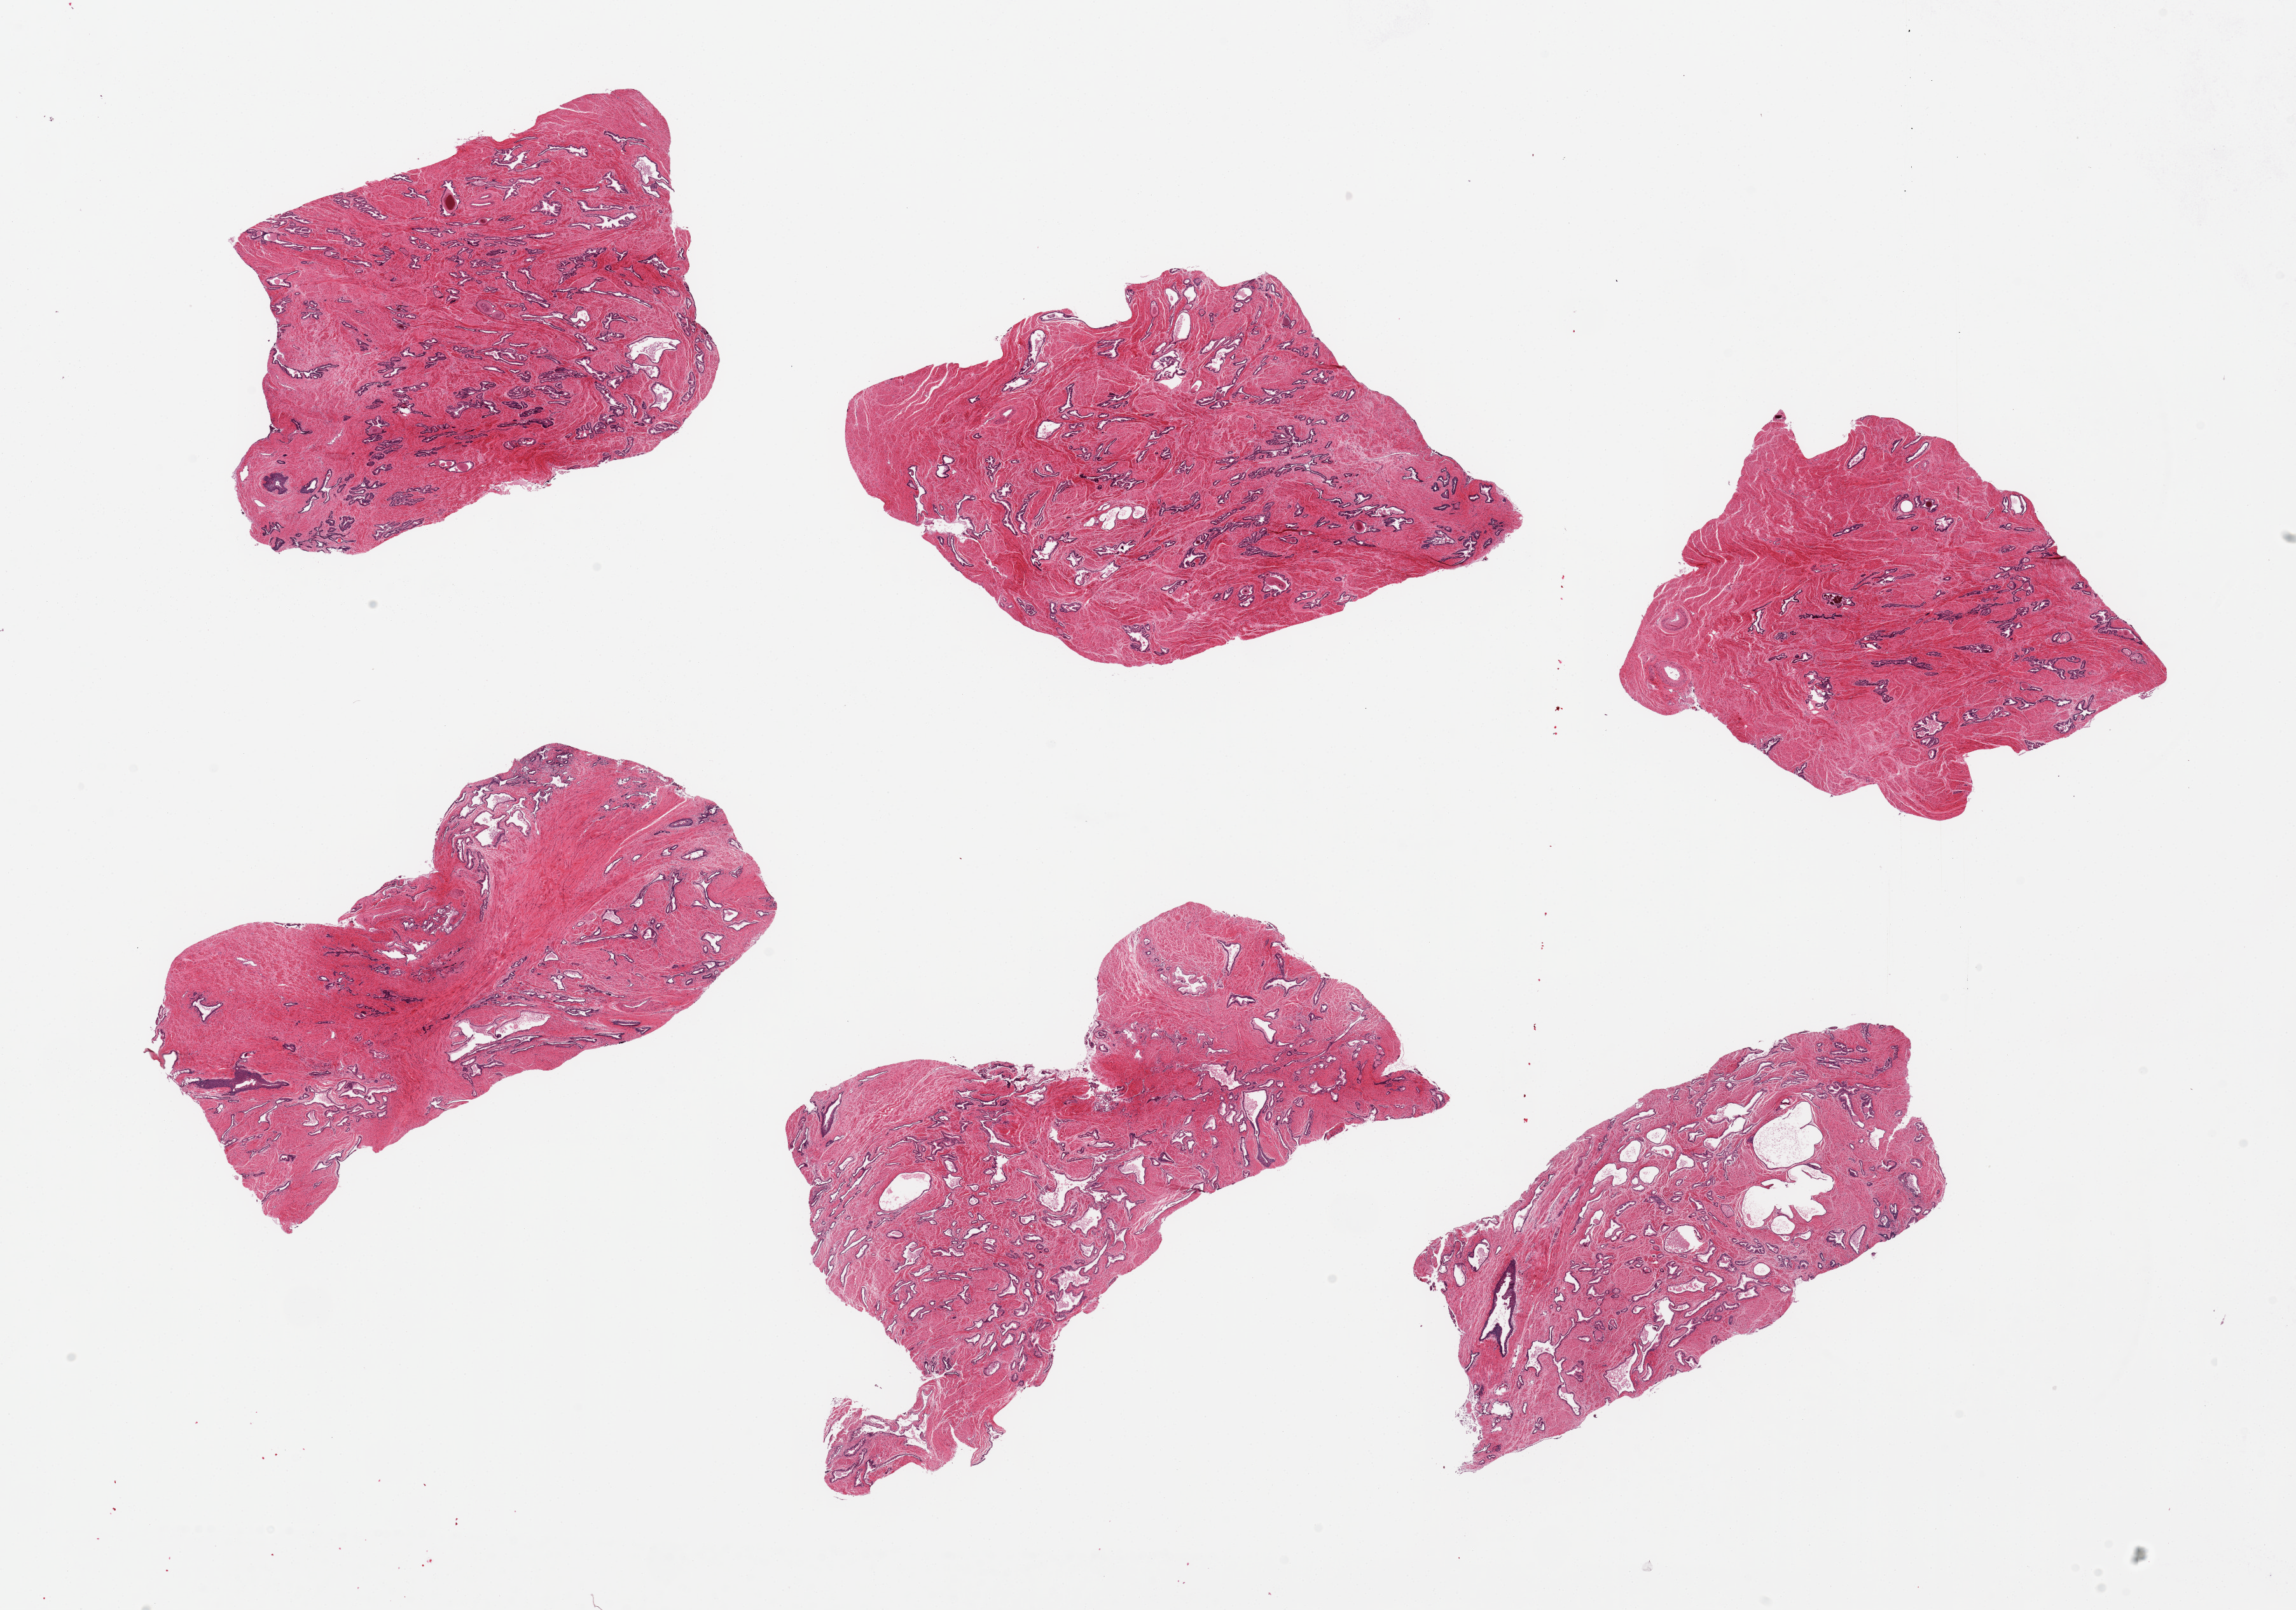
H&E whole-slide image — low-resolution overview of the scanned area, about 28.5 x 20.0 mm, PAXgene-fixed paraffin-embedded (PFPE) section, sampled site (target tissue): prostate, donor tissue sample. Male donor.
Review note (as recorded): 6 pieces; prostate NOT esophageal mucosa.